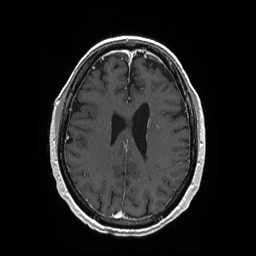
Brain MRI from a brain-tumour surgery series, one axial slice; T1-weighted post-contrast; 1 mm slice thickness; 256 × 256 image matrix, field of view 256 × 256 mm. From the clinical record (not read from this slice): histopathology: Primary diffuse large B-cell lymphoma.
Structures marked on this image (outlined manually by an expert reader):
- tumour: box from (x=156, y=125) to (x=160, y=129) px